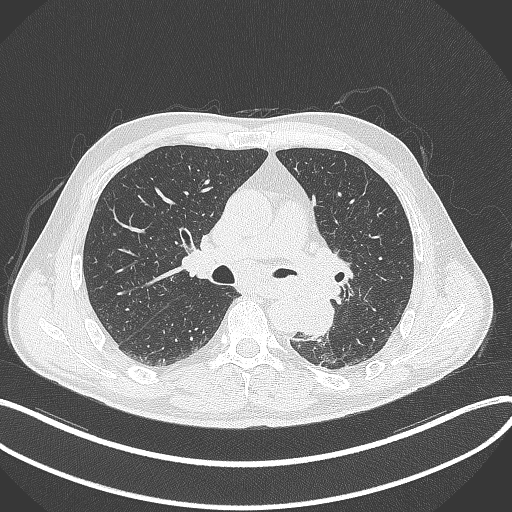
Chest CT, one axial slice. Position 202 of 329 along the scan axis. Reconstruction kernel B70f. 120 kVp. Lung window (W 1500 / L -600 HU). 512 × 512 image matrix, field of view 400 × 400 mm. Patient: male, 59 years. From the clinical record (not read from this slice): clinical TNM (as recorded): T2a N2 M0.
Annotated regions visible in this slice (bounding box drawn by a radiologist):
- lung tumour (recorded histology: squamous cell carcinoma): bounding box <296,286,337,339> (left, top, right, bottom; pixels)